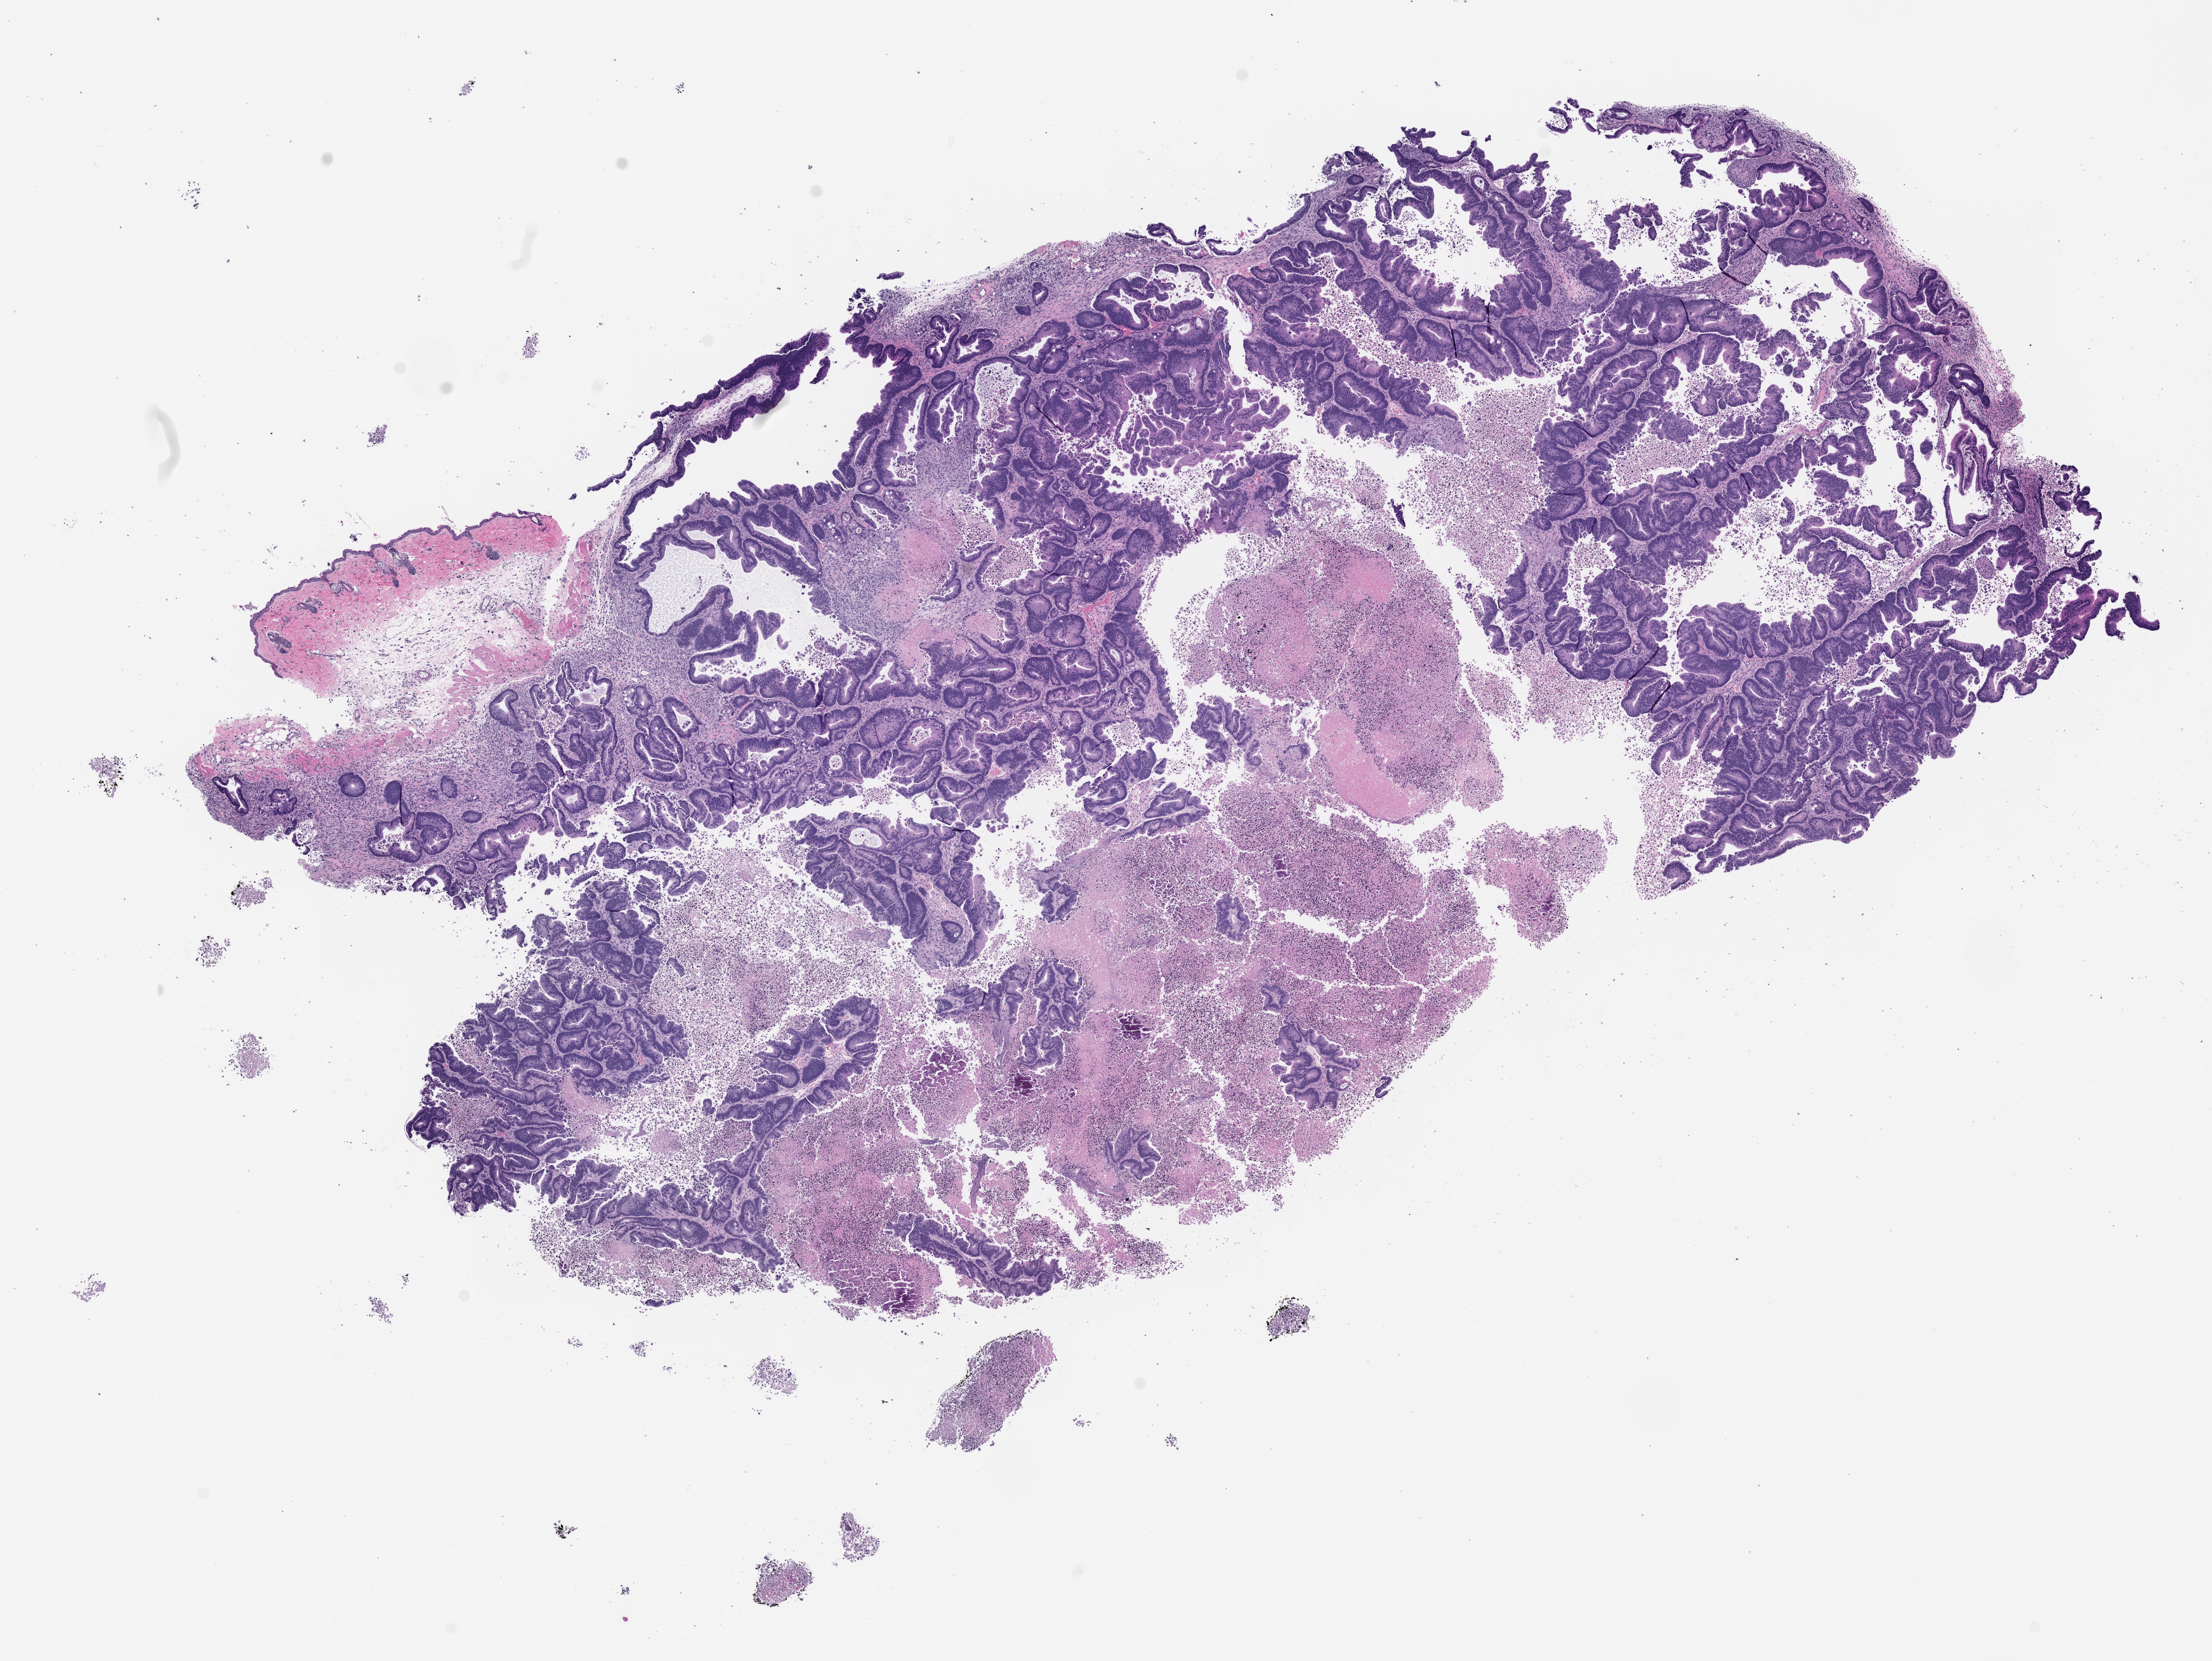
Whole-slide image, H&E: patient-derived xenograft (human tumor grown in a mouse), passage 1 — whole scanned area (about 14.0 x 10.5 mm) shown as a low-resolution overview; formalin-fixed paraffin-embedded section; tumor site category: gastrointestinal tract.
• originating patient diagnosis: Colorectal Carcinoma